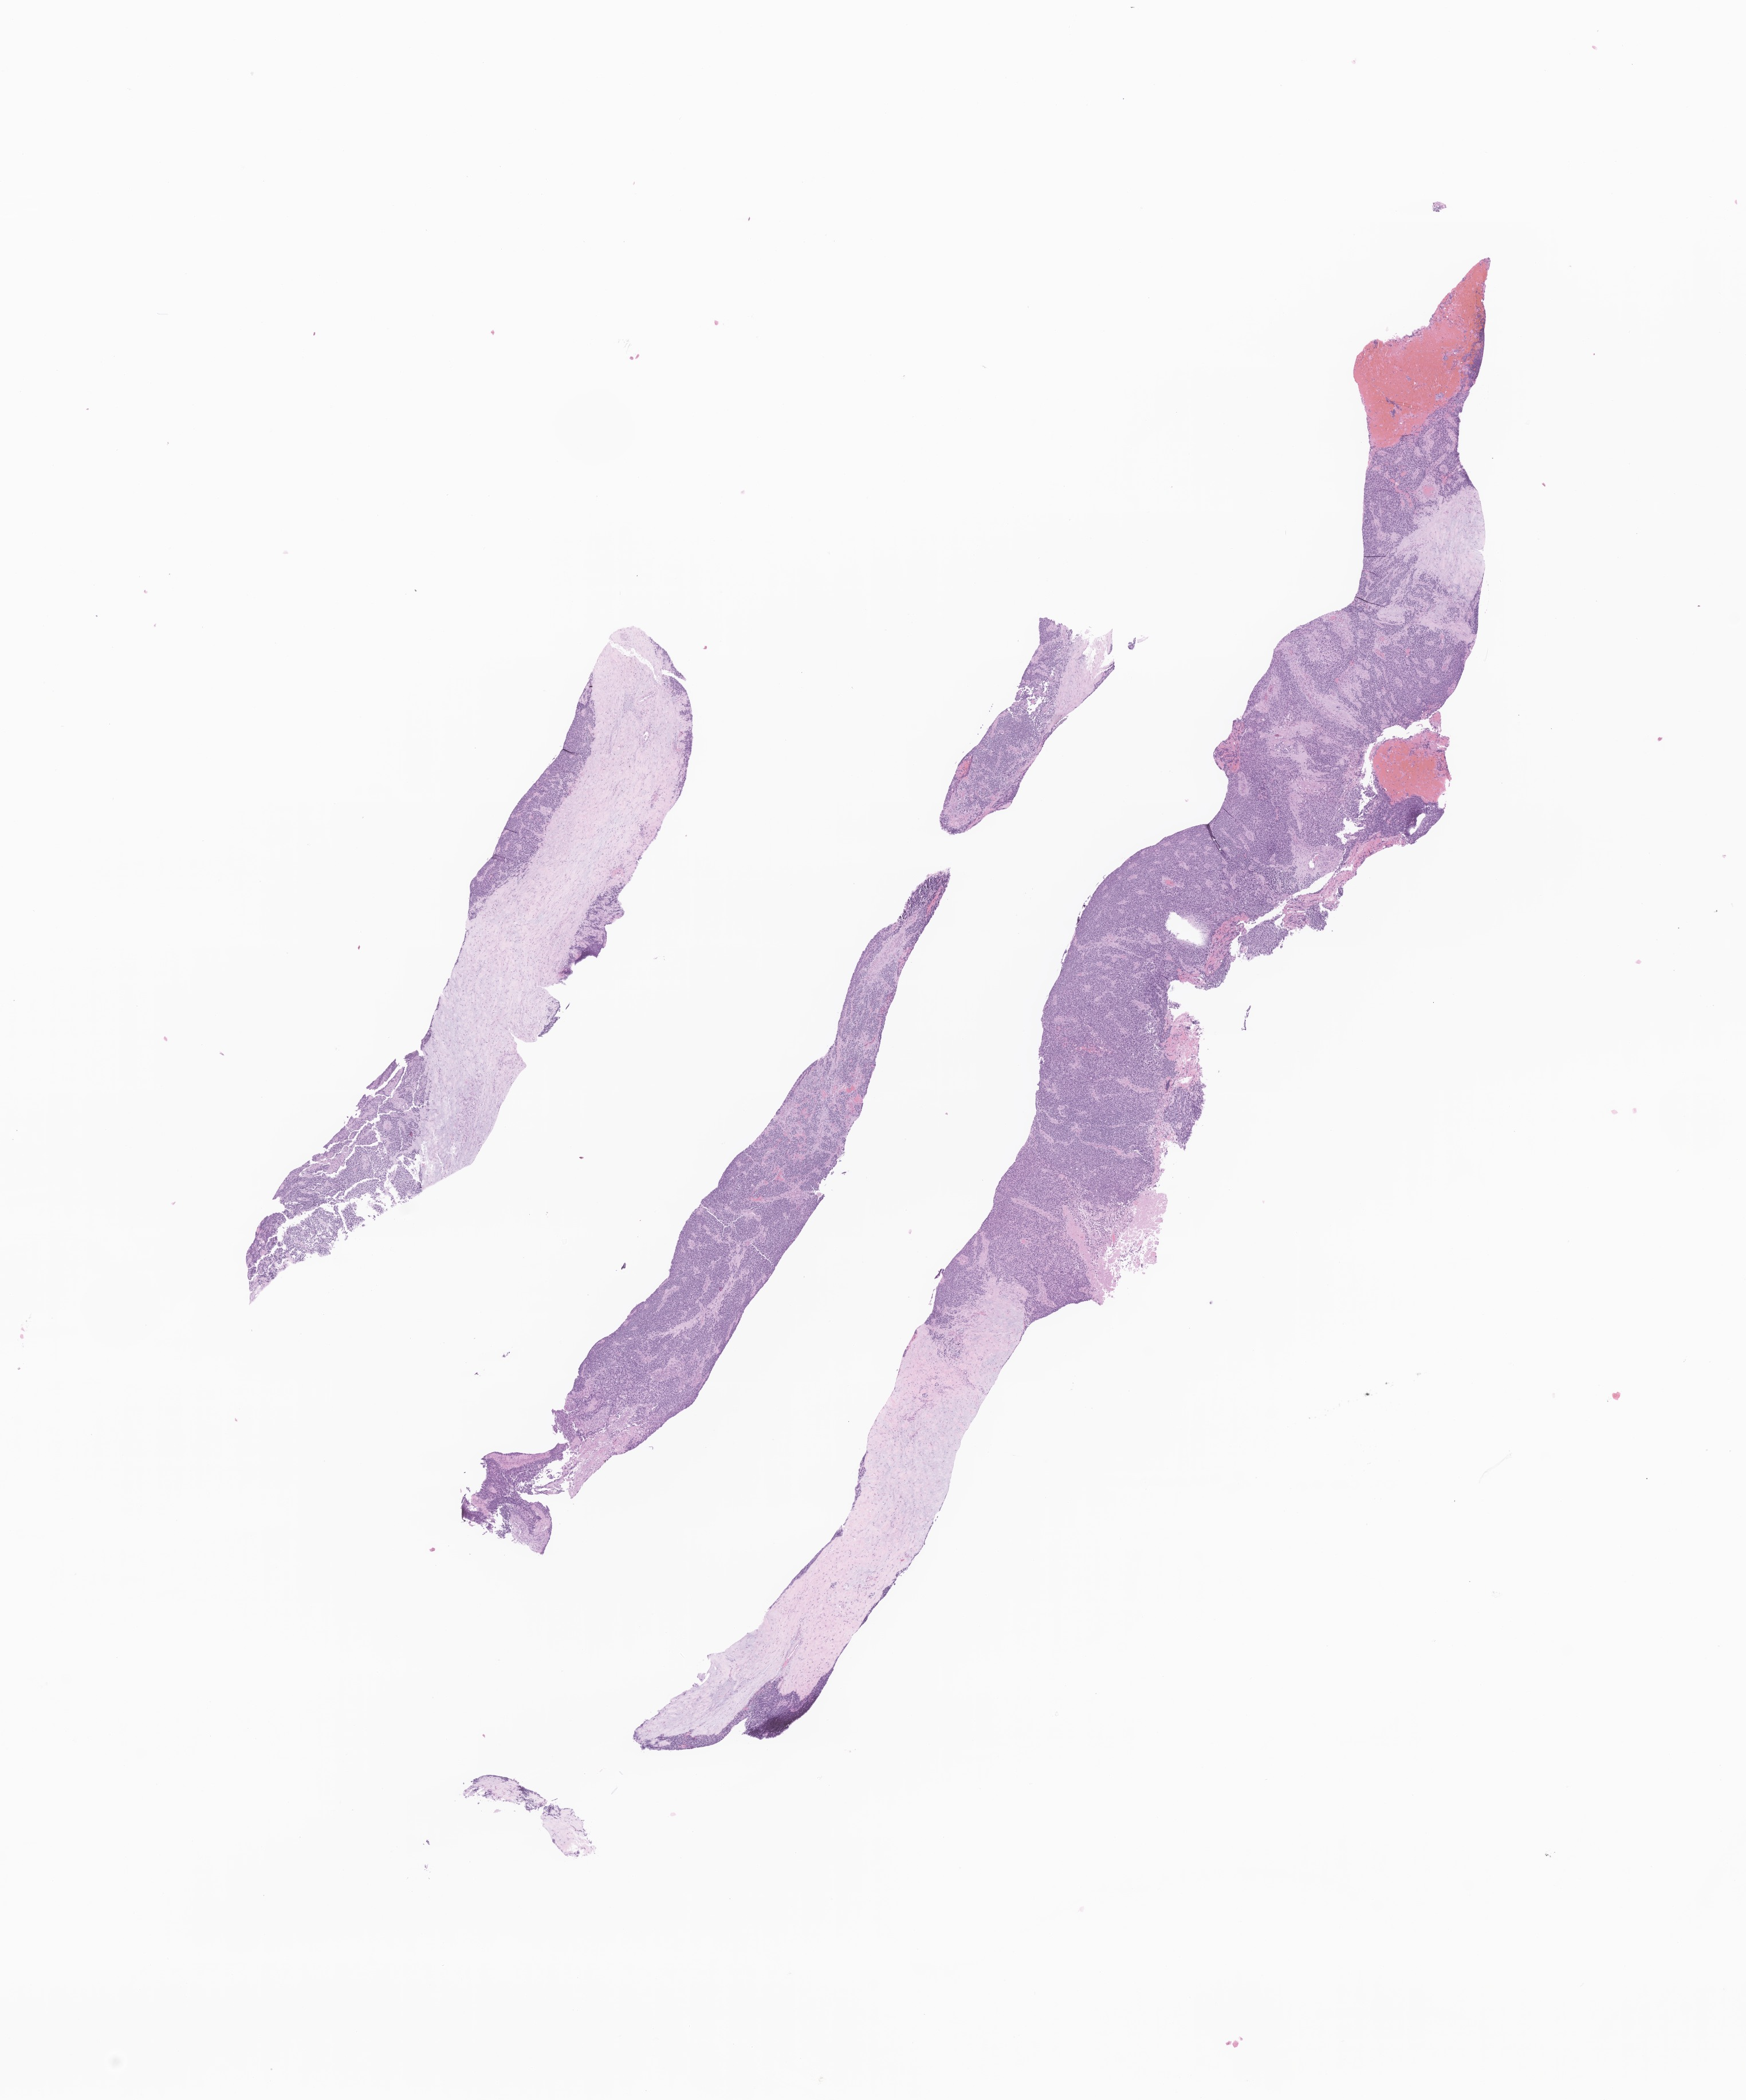
Hematoxylin and eosin (H&E) whole-slide image of tumor tissue from the retroperitoneum, shown as a low-resolution overview of the whole scanned area (about 12.9 x 15.5 mm). Formalin-fixed paraffin-embedded section. Patient female; age 821 days (about 2.2 years).
• diagnosis: Neuroblastoma, NOS